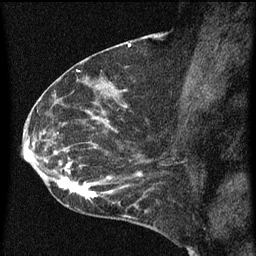
Breast MRI (dynamic contrast-enhanced), one sagittal slice. Position 37 of 60 along the scan axis. Dynamic contrast-enhanced series, image 2 of 3 at this slice position (ordered by acquisition). 1.5 T. TE 4.2 ms, TR 8 ms. 2 mm slice thickness. 256 × 256 image matrix, field of view 180 × 180 mm. Female patient, age 54 years.
Annotated regions visible in this slice (semi-automatic segmentation, software-assisted and operator-edited):
- analysis volume of interest (the breast-tissue region the enhancement analysis was run in; not a lesion): box from (x=49, y=138) to (x=164, y=209) px
- tumour enhancement mask (voxels above the 70 % enhancement threshold inside the analysis volume of interest): (x=49, y=142)–(x=146, y=209)